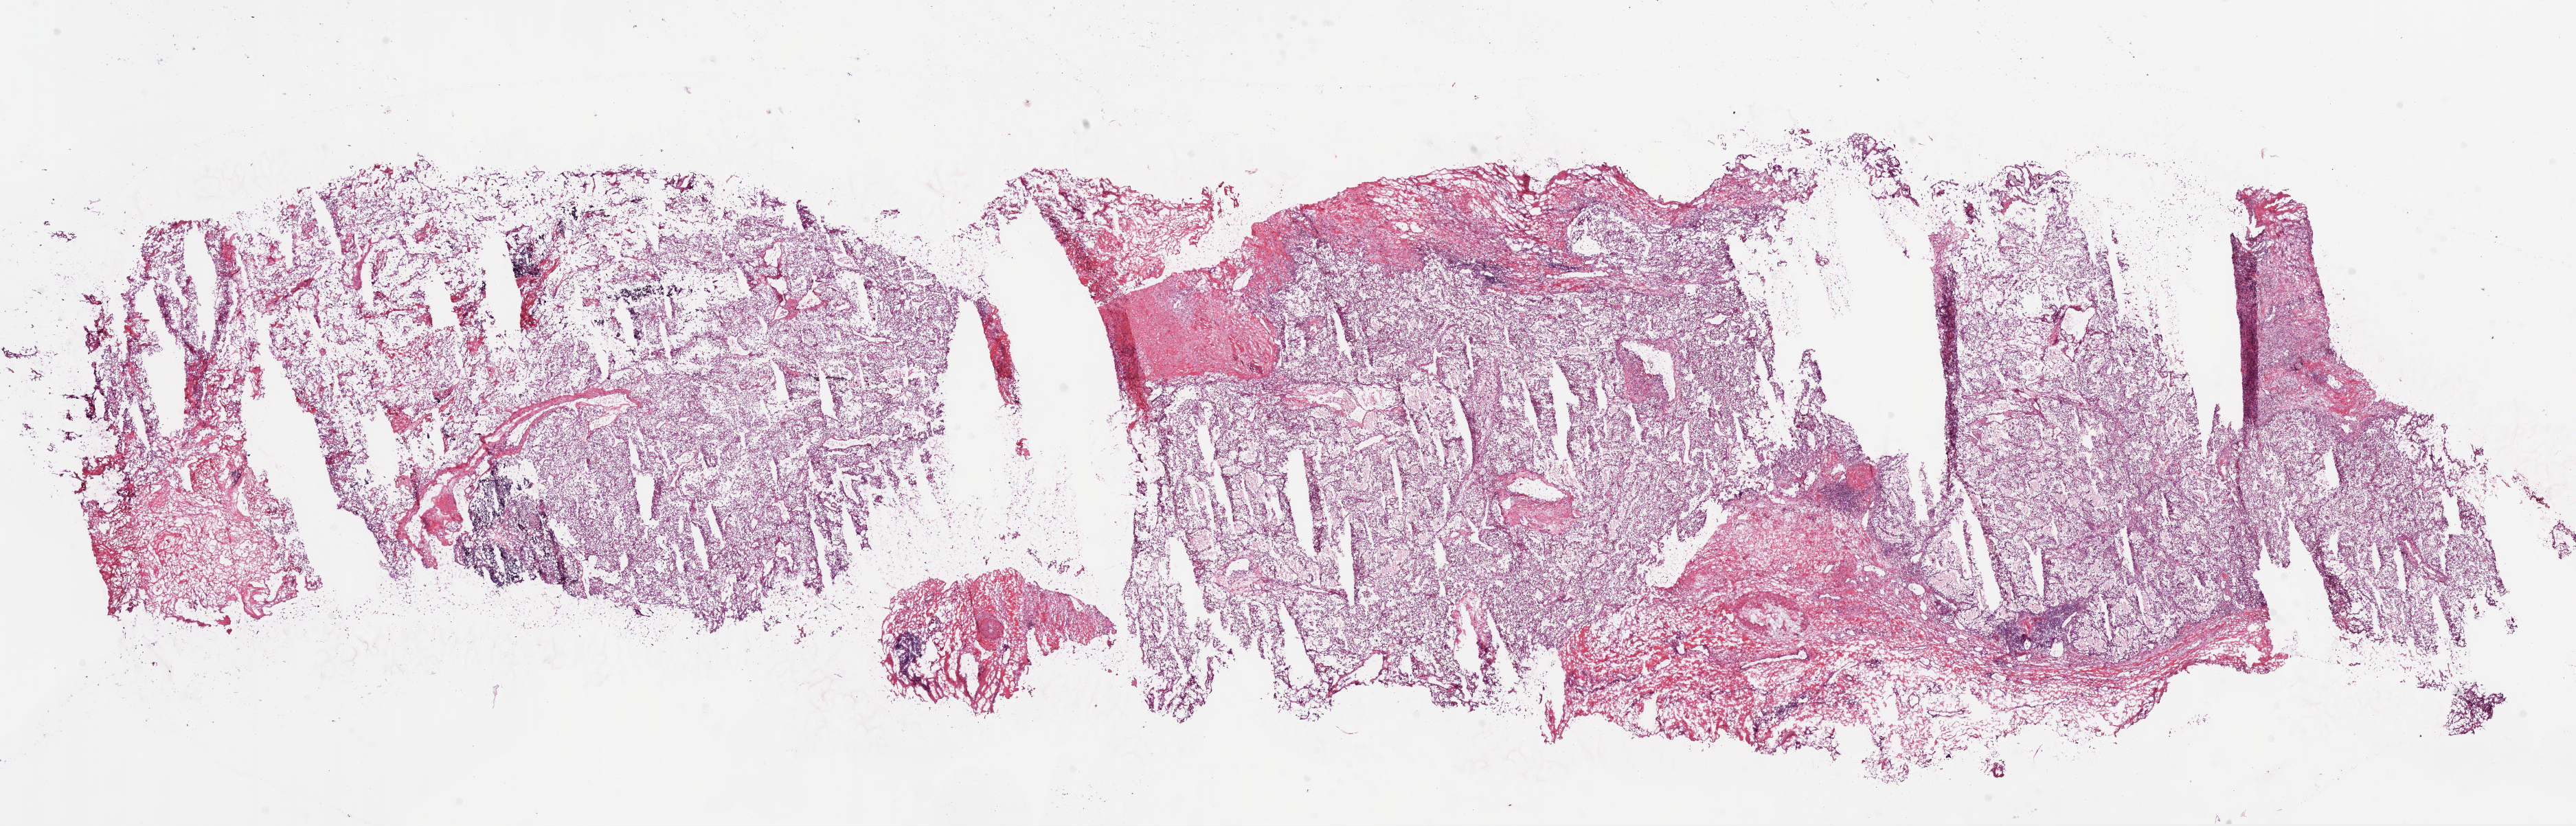
H&E whole-slide image, low-resolution overview of the scanned area, about 30.1 x 9.7 mm, frozen section from the bottom of the tissue portion, kidney, primary tumour sample. Patient: male, age at initial diagnosis 61 years. Histologic grade: G3 (poorly differentiated). Slide review estimates, as recorded: tumour cells 80%, tumour nuclei 75%, normal cells 0%, stromal cells 20%, necrosis 0%.
AJCC pathologic stage: III. Histologic diagnosis: Clear cell adenocarcinoma, NOS.